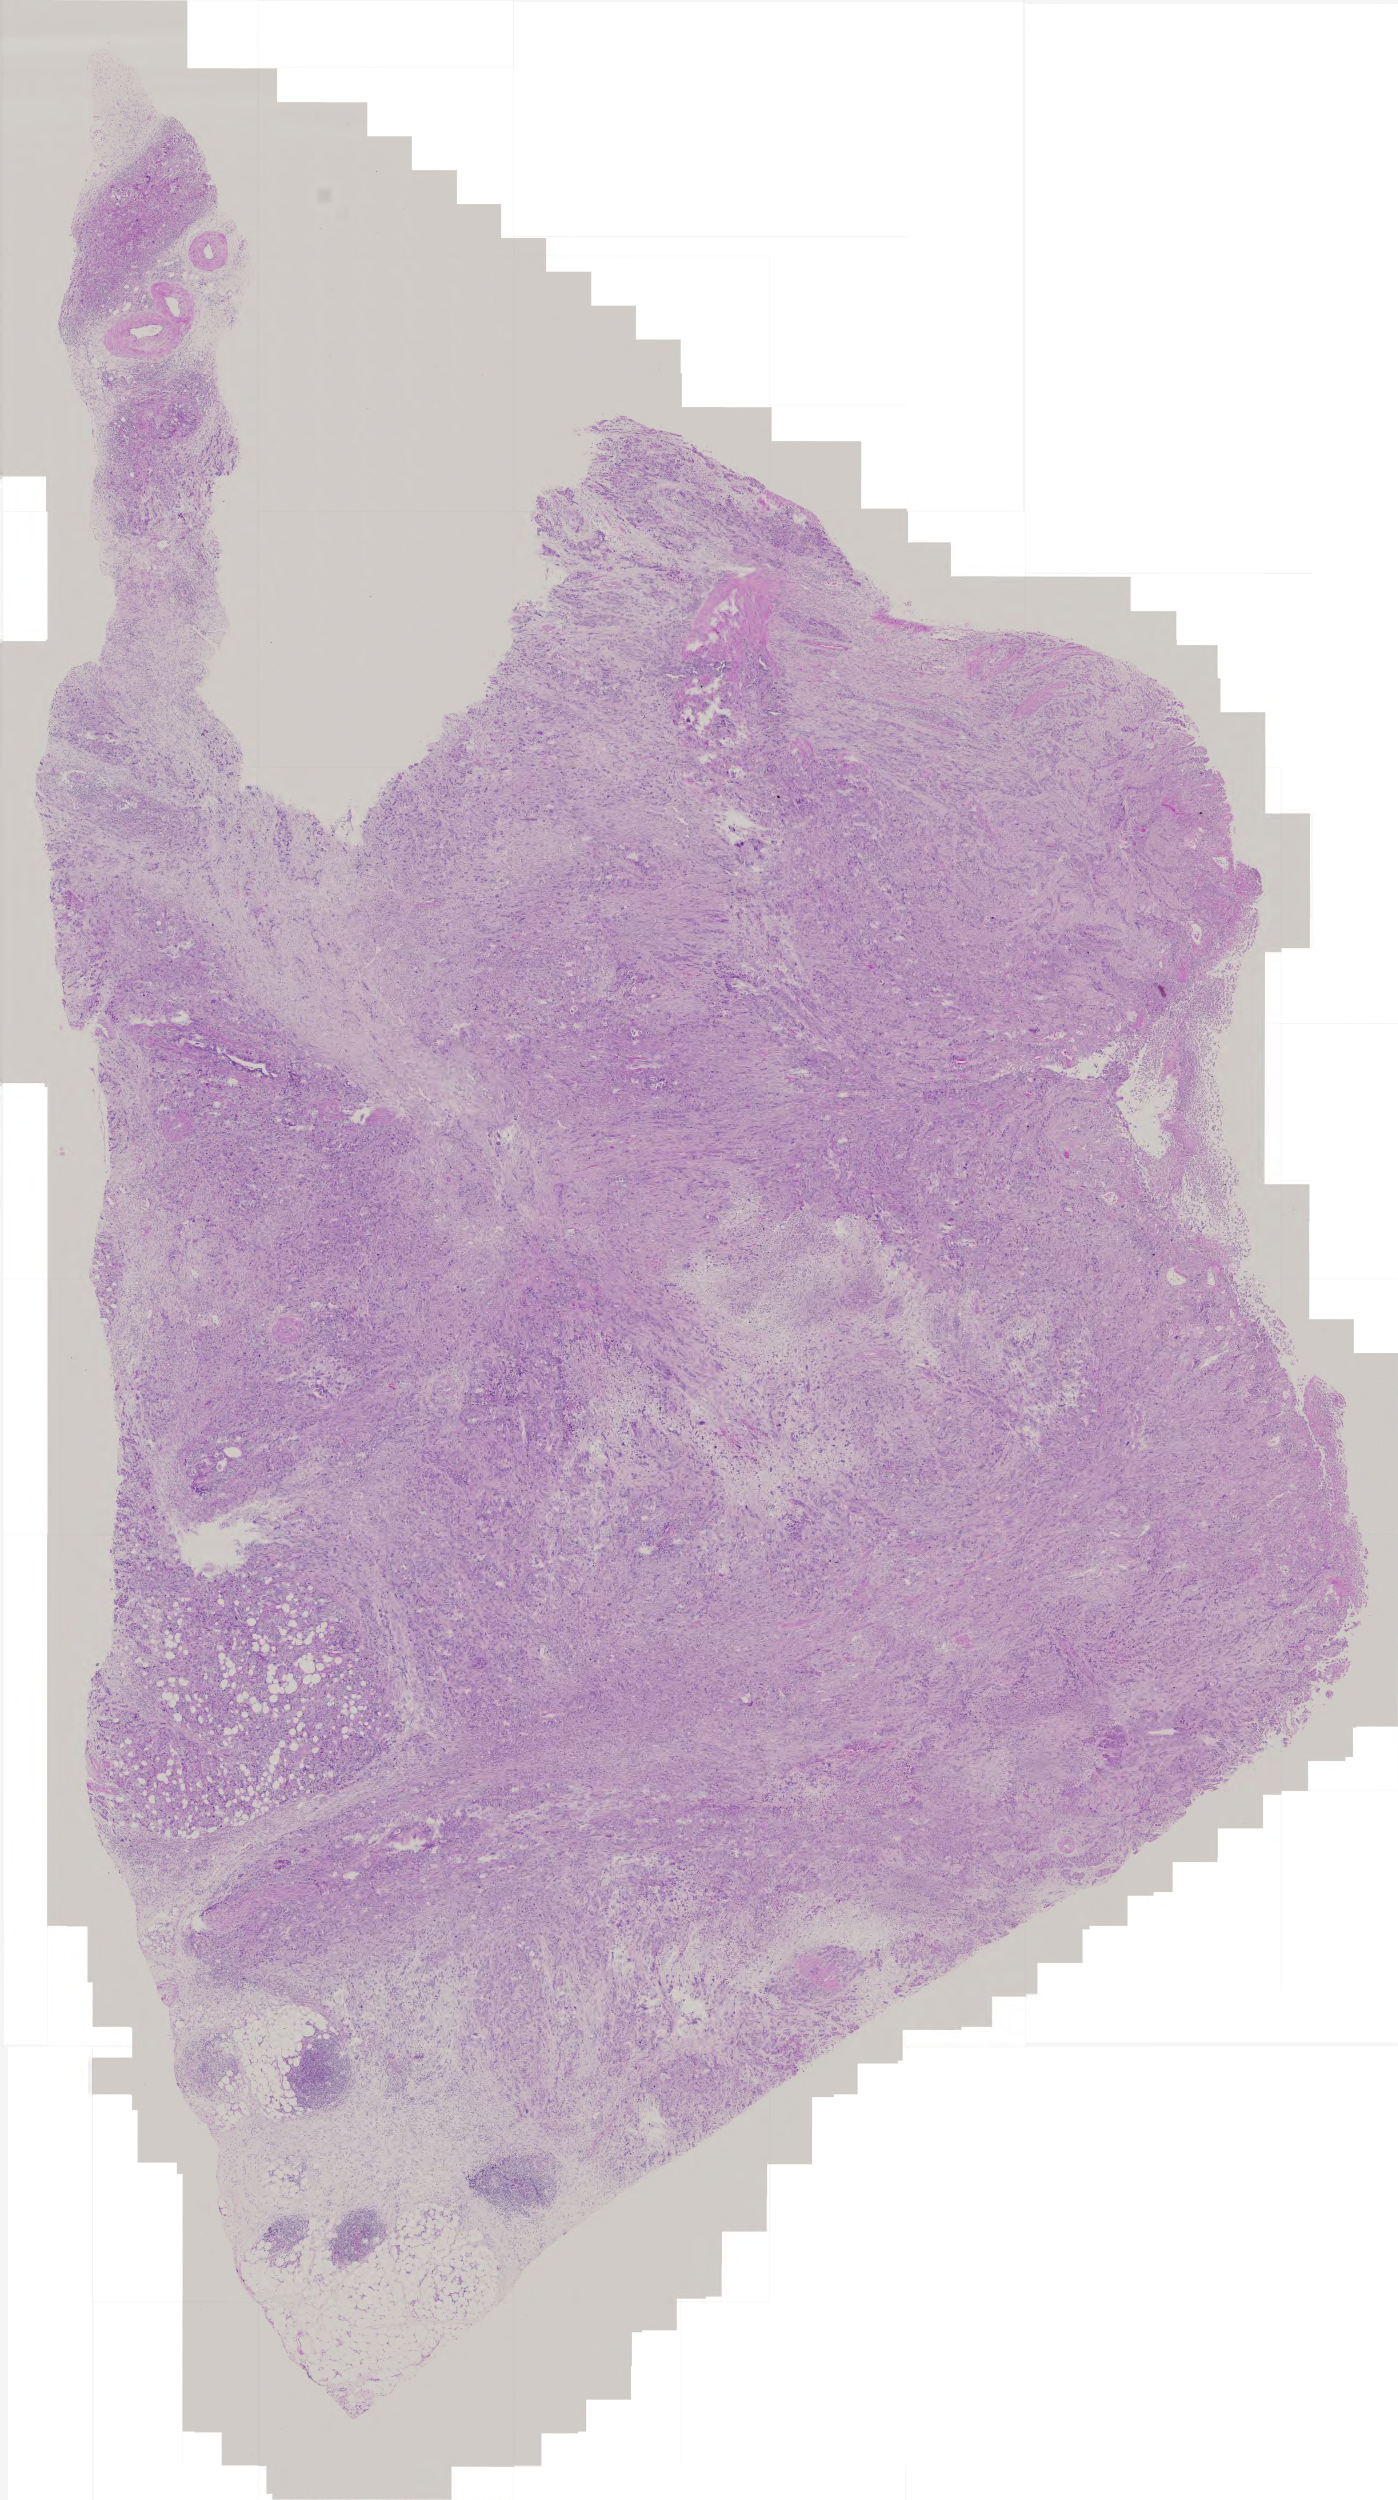
Whole-slide histology image, H&E-stained — low-resolution overview of the scanned area, about 2.8 x 5.0 mm, formalin-fixed paraffin-embedded (FFPE) diagnostic section, primary tumour sample from the stomach. Male patient; age at initial diagnosis 59 years. Histologic grade: G3 (poorly differentiated).
• lymph nodes positive (case pathology): 34 of 40 examined
• AJCC pathologic stage: IV
• pathologic diagnosis: Carcinoma, diffuse type